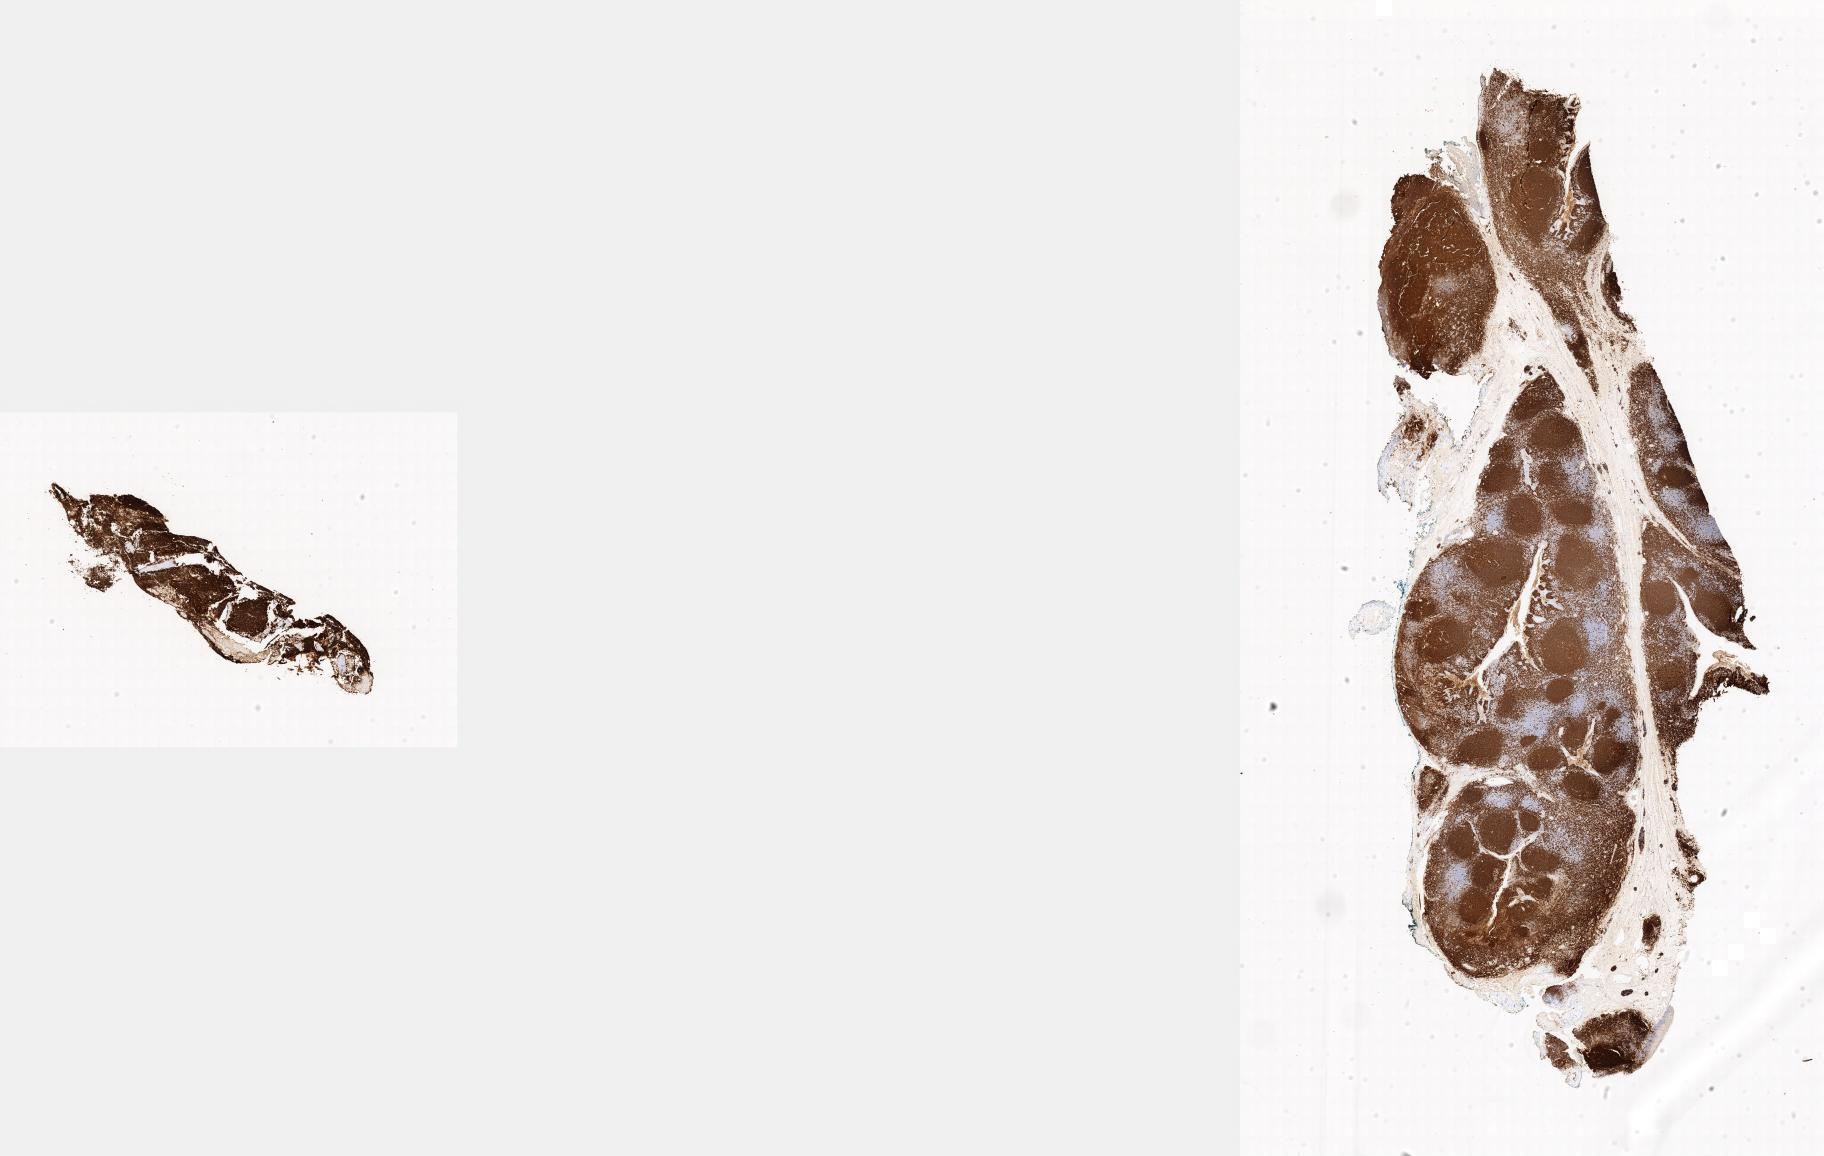
IHC for CD20, whole-slide image — low-resolution overview of the scanned area, specimen: tumor tissue, anatomic site: bone marrow. Female patient; age at initial diagnosis 3 years.
- diagnosis: Burkitt lymphoma, NOS